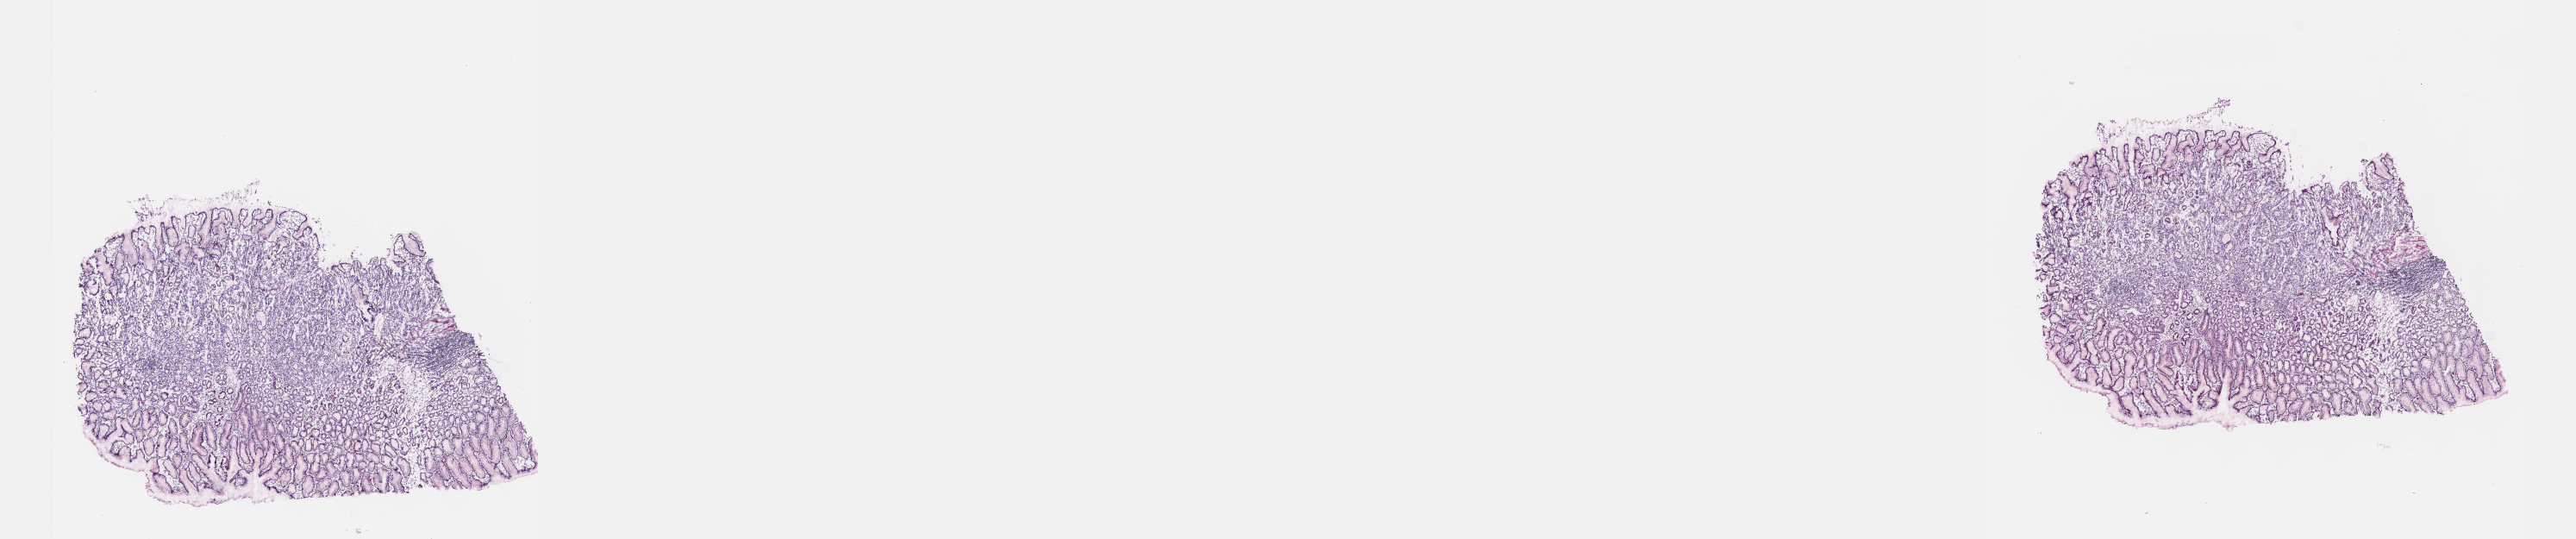
Whole-slide histology image, Hematoxylin and eosin (H&E) stained — low-resolution overview of the scanned area, about 24.1 x 5.0 mm. Frozen section. Primary tumour sample from the stomach. Patient: male, age at initial diagnosis 45 years.
Histologic diagnosis: Mucinous adenocarcinoma (gastric antrum).